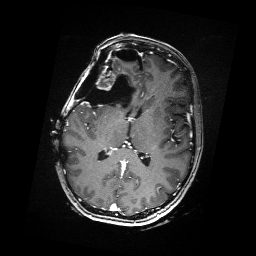
Brain MRI from a brain-tumour surgery series, one axial slice. Slice 87 of 176 in the series (ordered by position). T1-weighted post-contrast. 256 × 256 image matrix, field of view 256 × 256 mm. Case-level facts recorded for this patient, not image findings: histopathology: Metastatic Carcinoma from Breast primary; tumour location: Right Frontal.
Structures marked on this image (expert manual segmentation):
- residual tumour: box from (x=88, y=68) to (x=117, y=88) px